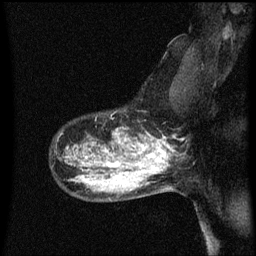
Breast MRI (dynamic contrast-enhanced), one sagittal slice; slice 46 of 60 in the series (ordered by position); dynamic contrast-enhanced series, image 2 of 3 at this slice position (ordered by acquisition); 1.5 T; TE 4.2 ms, TR 8.4 ms; 2 mm slice thickness; 256 × 256 image matrix. Female patient, age 50 years.
Annotated regions visible in this slice (semi-automatically segmented with operator editing):
- analysis volume of interest (the breast-tissue region the enhancement analysis was run in; not a lesion): bounding box [x1, y1, x2, y2] px = [100, 116, 153, 171]
- tumour enhancement mask (voxels above the 70 % enhancement threshold inside the analysis volume of interest): [107, 134, 153, 171]